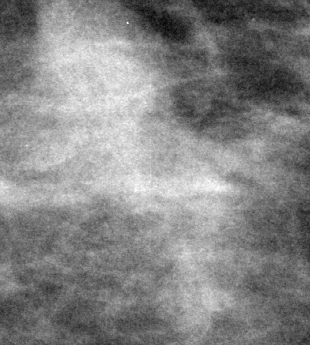
Region of interest cut from a scanned film mammogram (one marked finding); left breast; MLO view; BI-RADS breast density category 2 (scale 1–4).
- Marked abnormality: mass, shape irregular, margins ill defined; BI-RADS assessment category 4; subtlety rating 4 on a 1 (subtle) to 5 (obvious) scale; pathology (as recorded): benign.